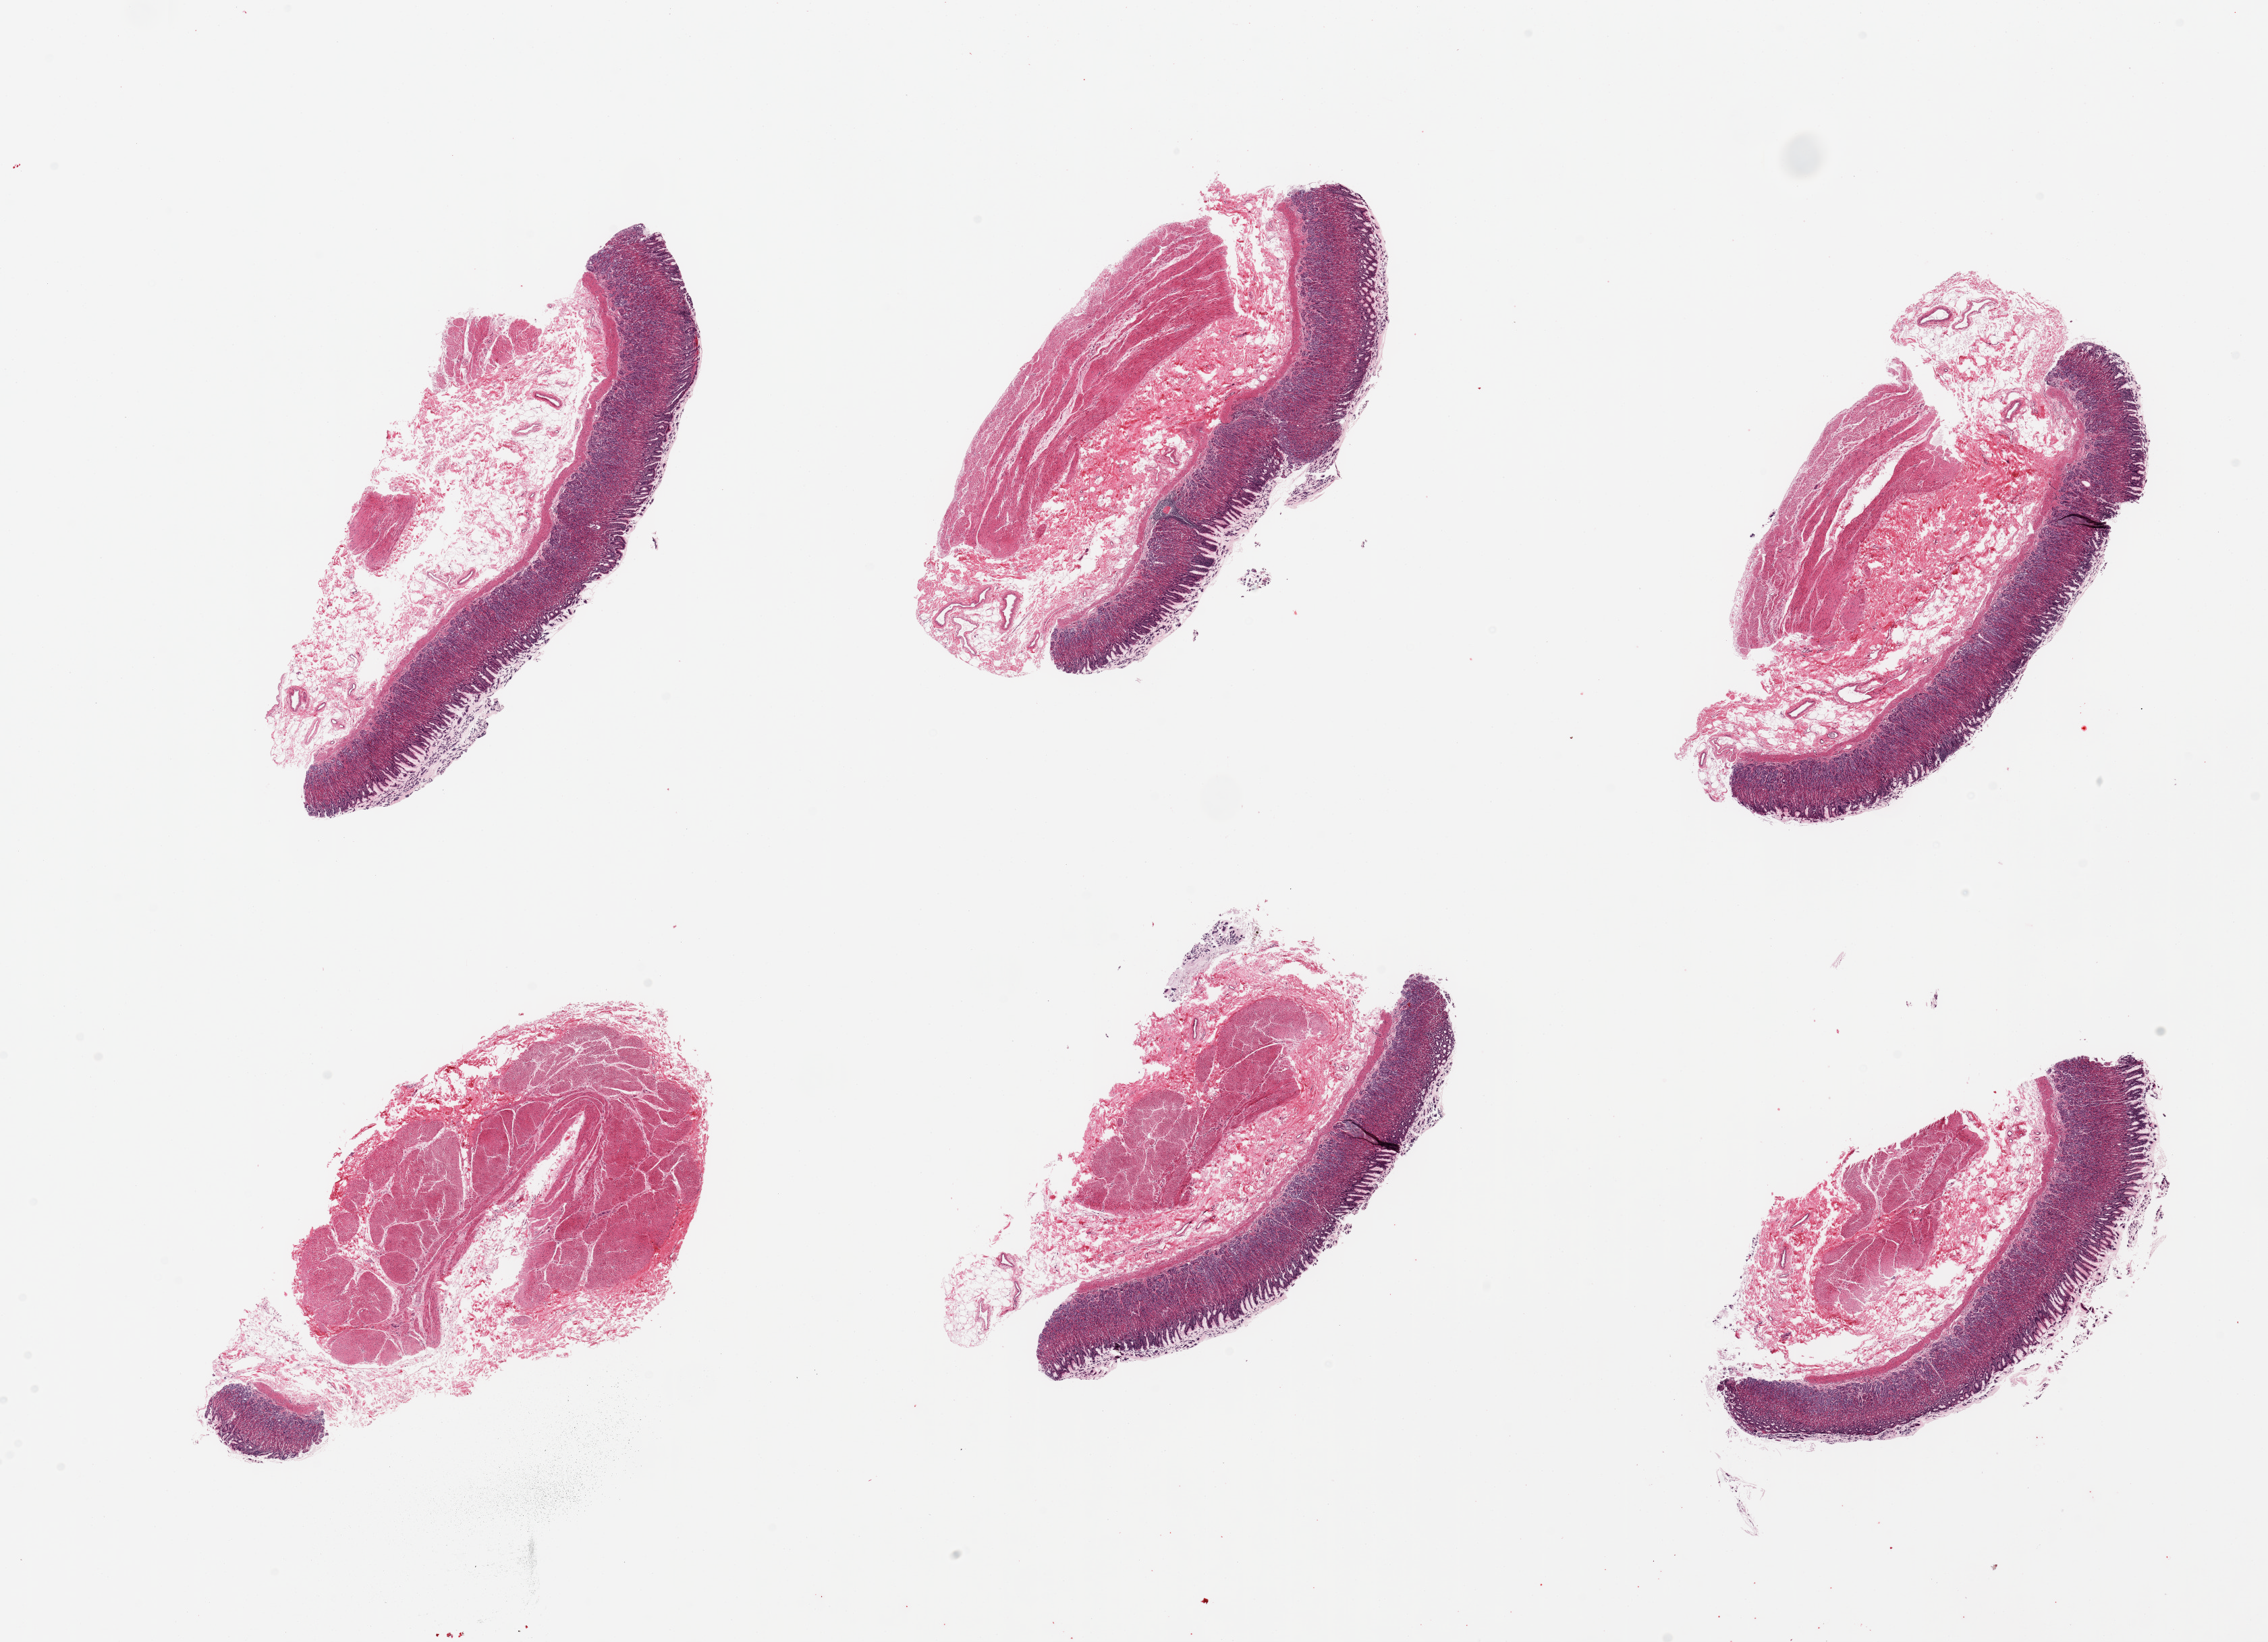
Whole-slide image, H&E stain — a low-resolution overview of the entire scanned area, about 26.6 x 19.2 mm; PAXgene-fixed paraffin-embedded (PFPE) section; sampled site (target tissue): stomach; donor tissue sample. Donor sex: male.
Review note (as recorded): 6 pieces, mucosa is ~1mm, 20-30% of thickness.